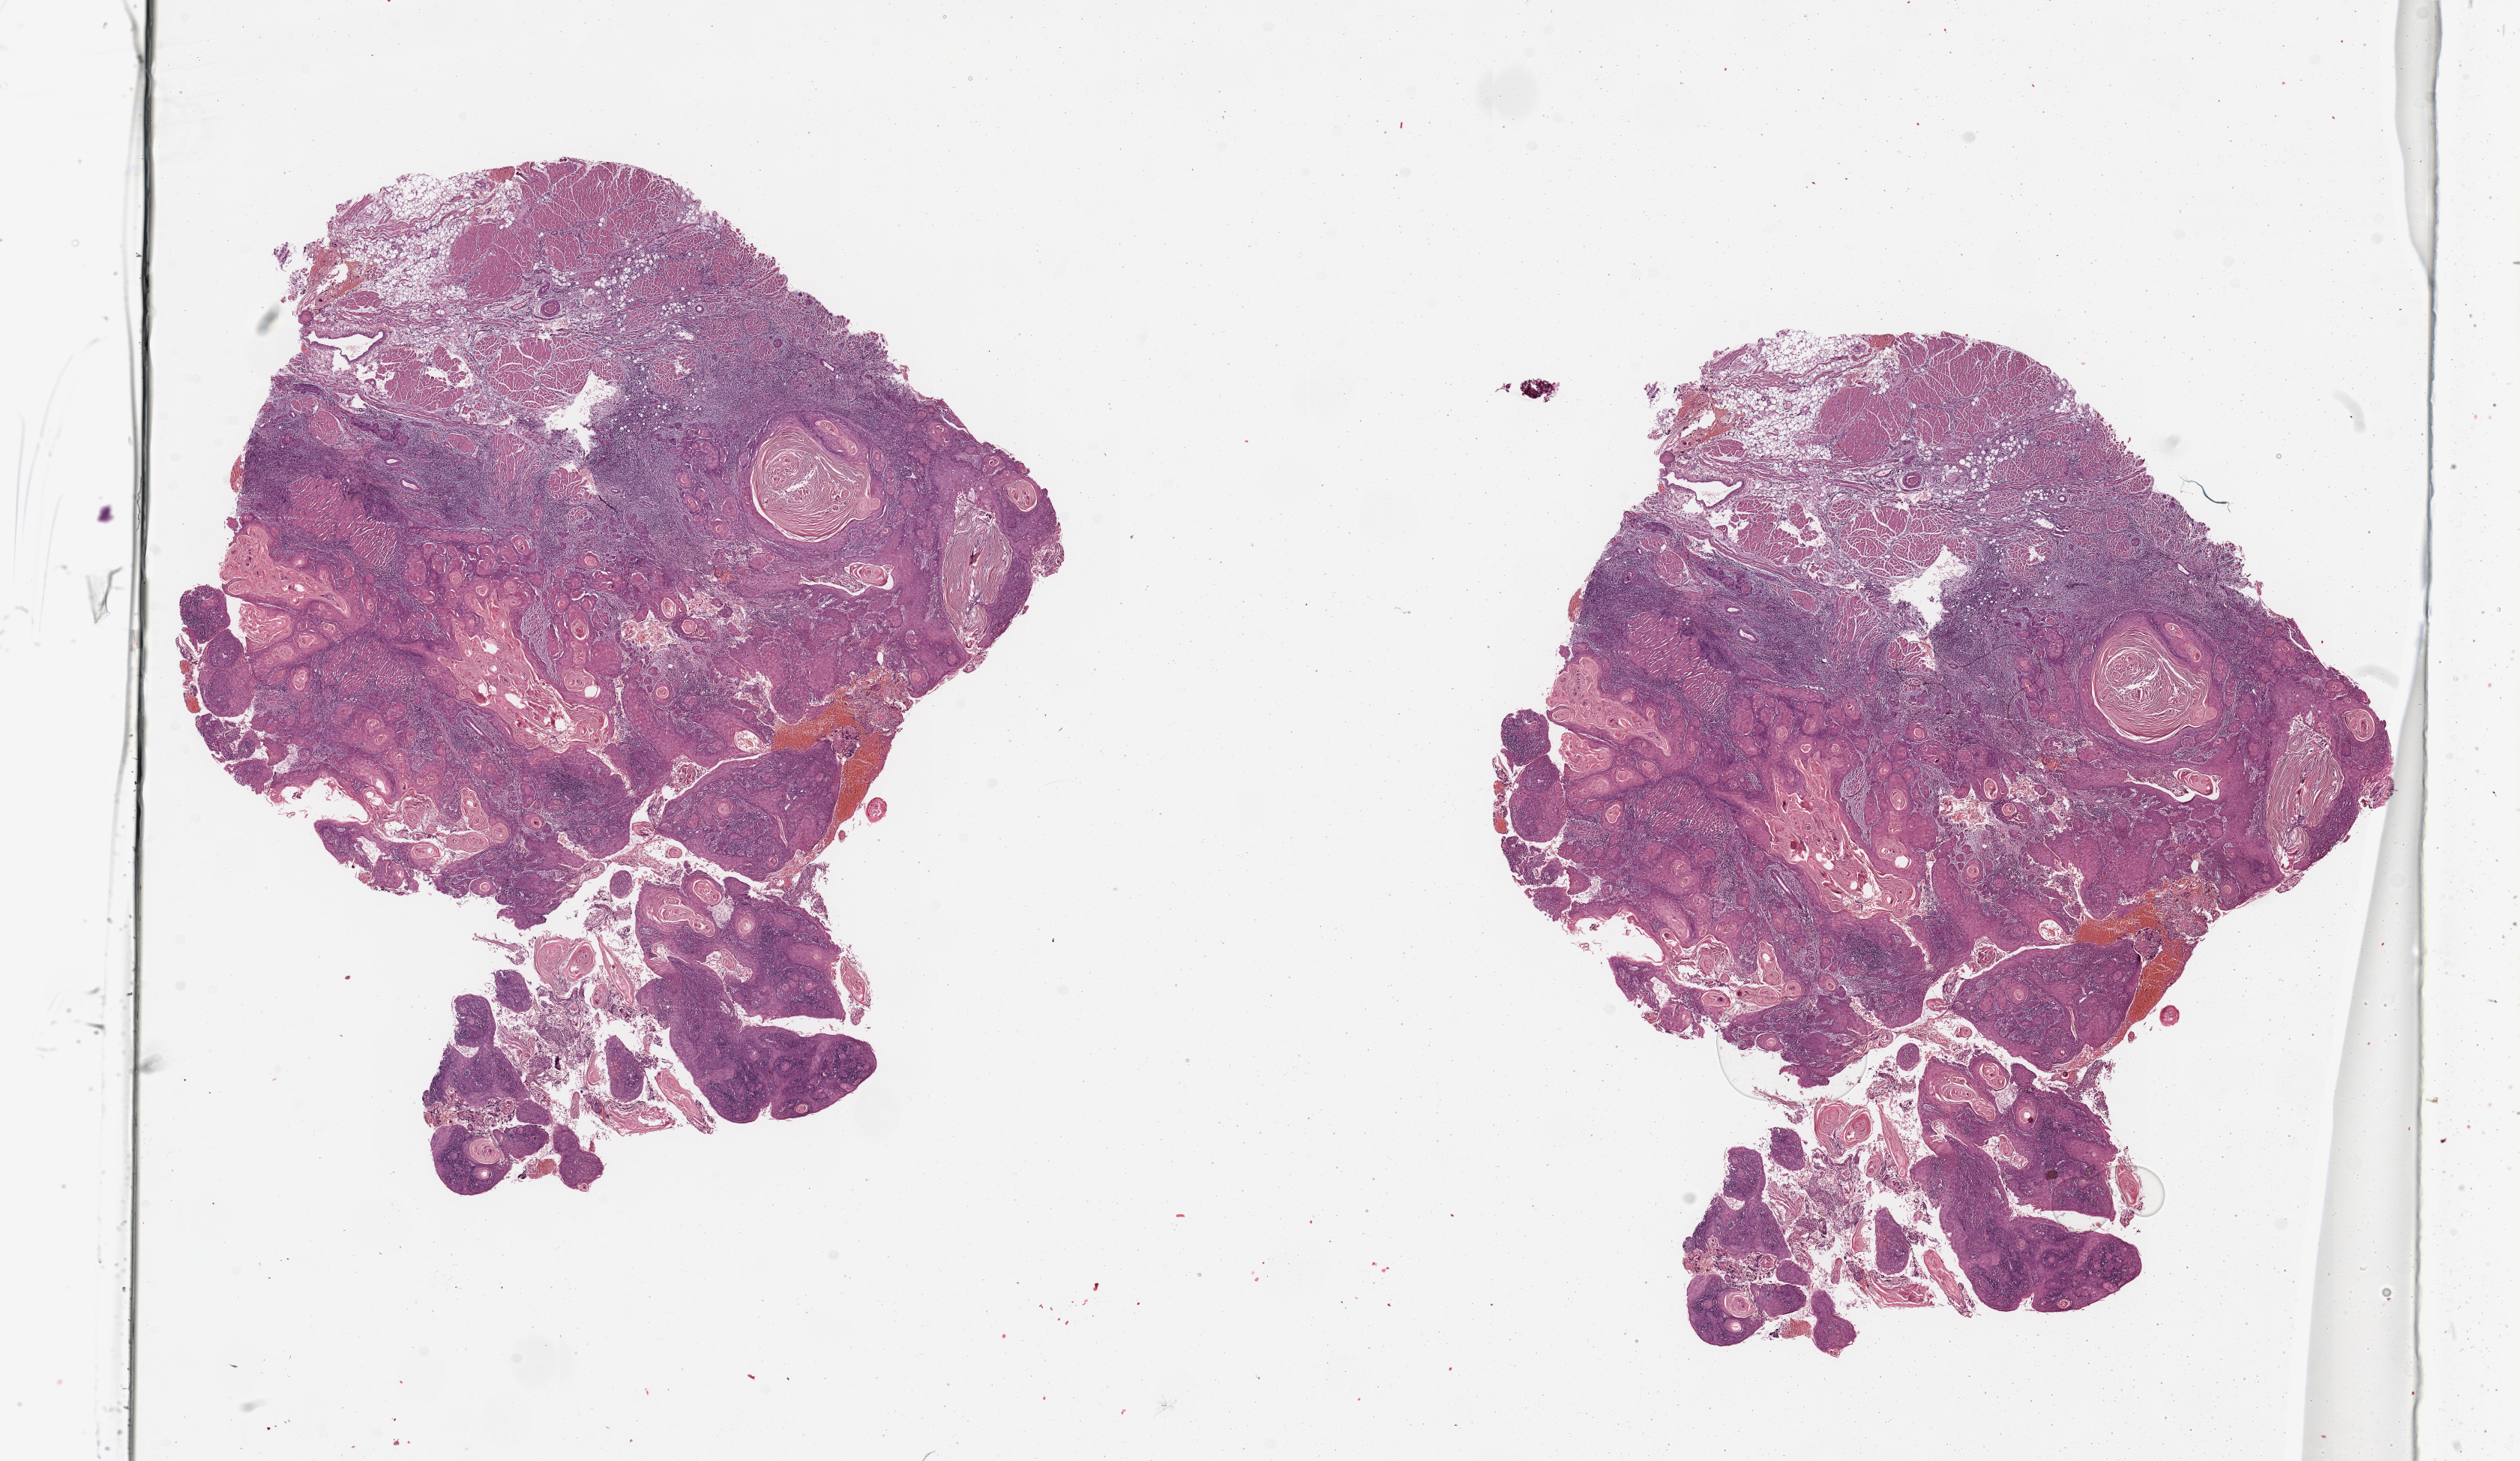
Whole-slide histology image, H&E — low-resolution overview of the scanned area, about 26.6 x 15.4 mm (slide scanned at 20x); head and neck, tissue type not recorded. Patient: female, age 60 years.
Patient diagnosis: Squamous cell carcinoma, NOS.